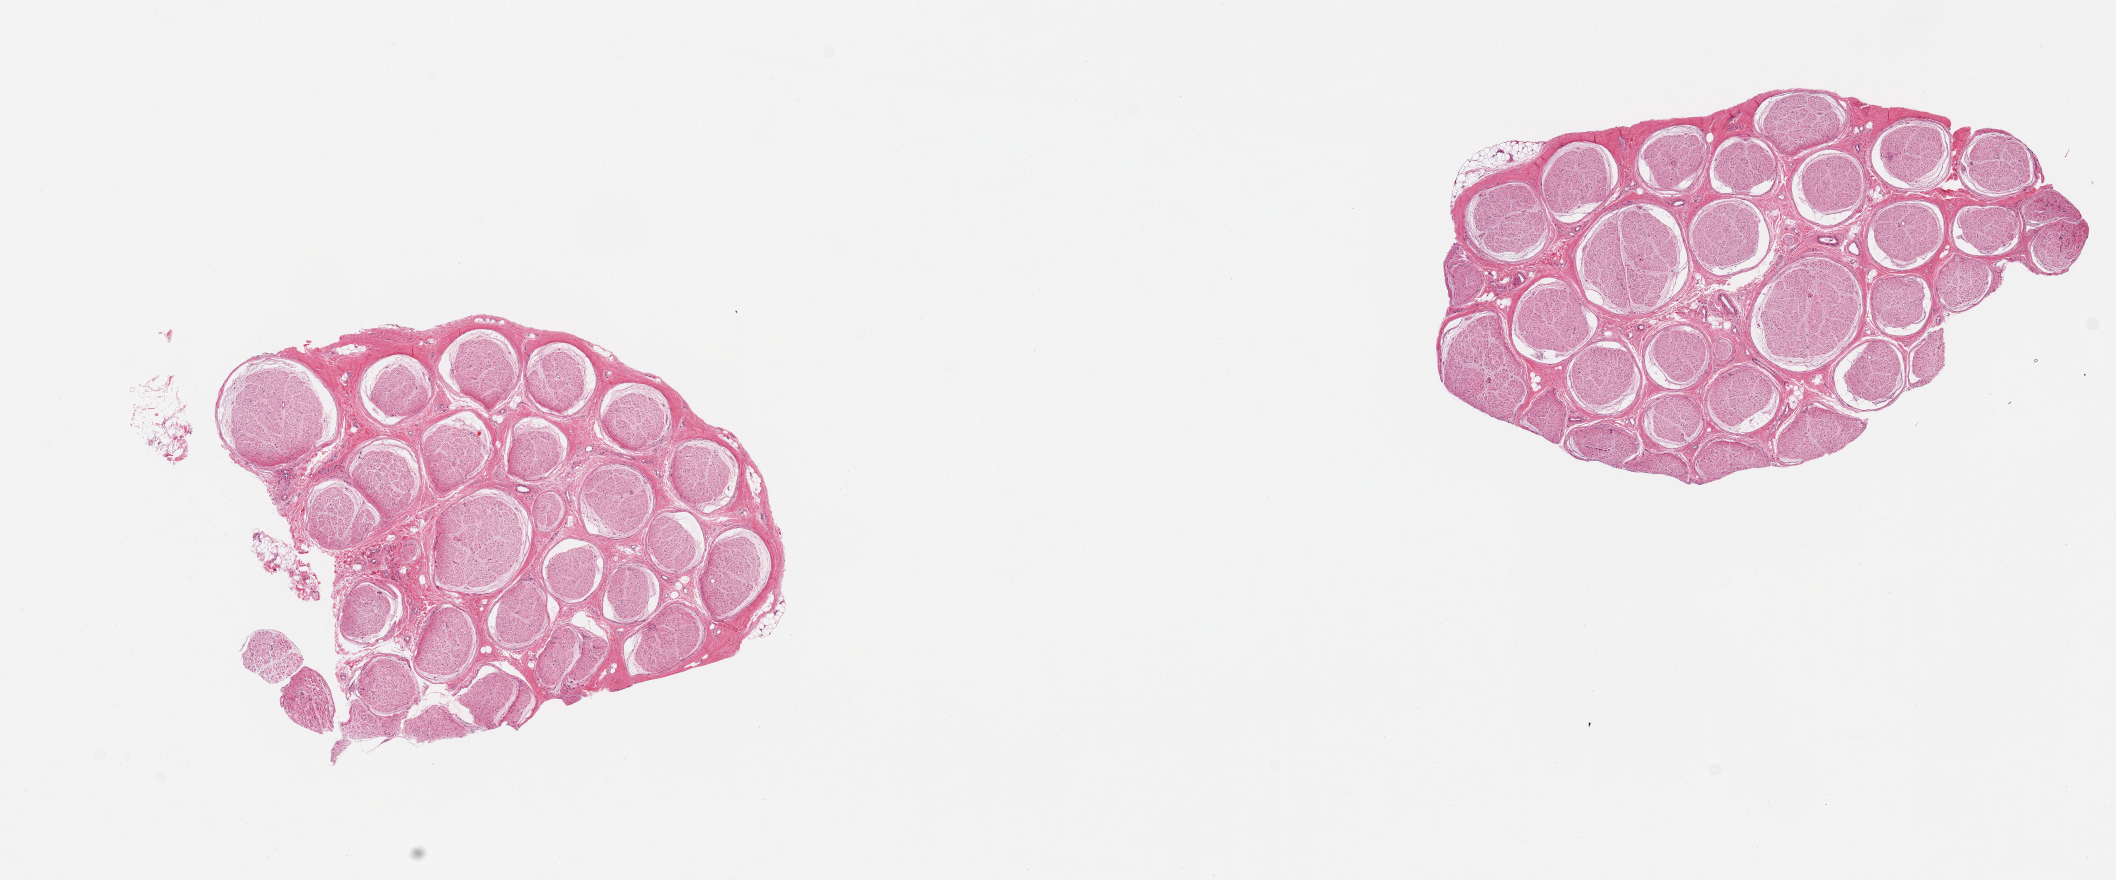
Hematoxylin and eosin (H&E) whole-slide image — a low-resolution overview of the entire scanned area, about 16.7 x 7.0 mm. PAXgene-fixed paraffin-embedded (PFPE) section. Sampled site (target tissue): tibial nerve. Tissue donor sample. Female donor.
Reviewer comment on this tissue sample: 2 pieces; well trimmed.